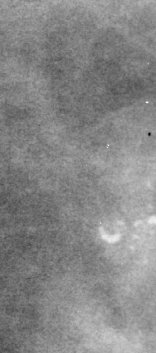
Crop from a digitized film mammogram around one marked abnormality; right breast; CC view; BI-RADS breast density category 2 (scale 1–4).
- Finding: calcifications, morphology pleomorphic, distribution clustered; BI-RADS assessment category 4; subtlety rating 4 on a 1 (subtle) to 5 (obvious) scale; pathology (as recorded): malignant.